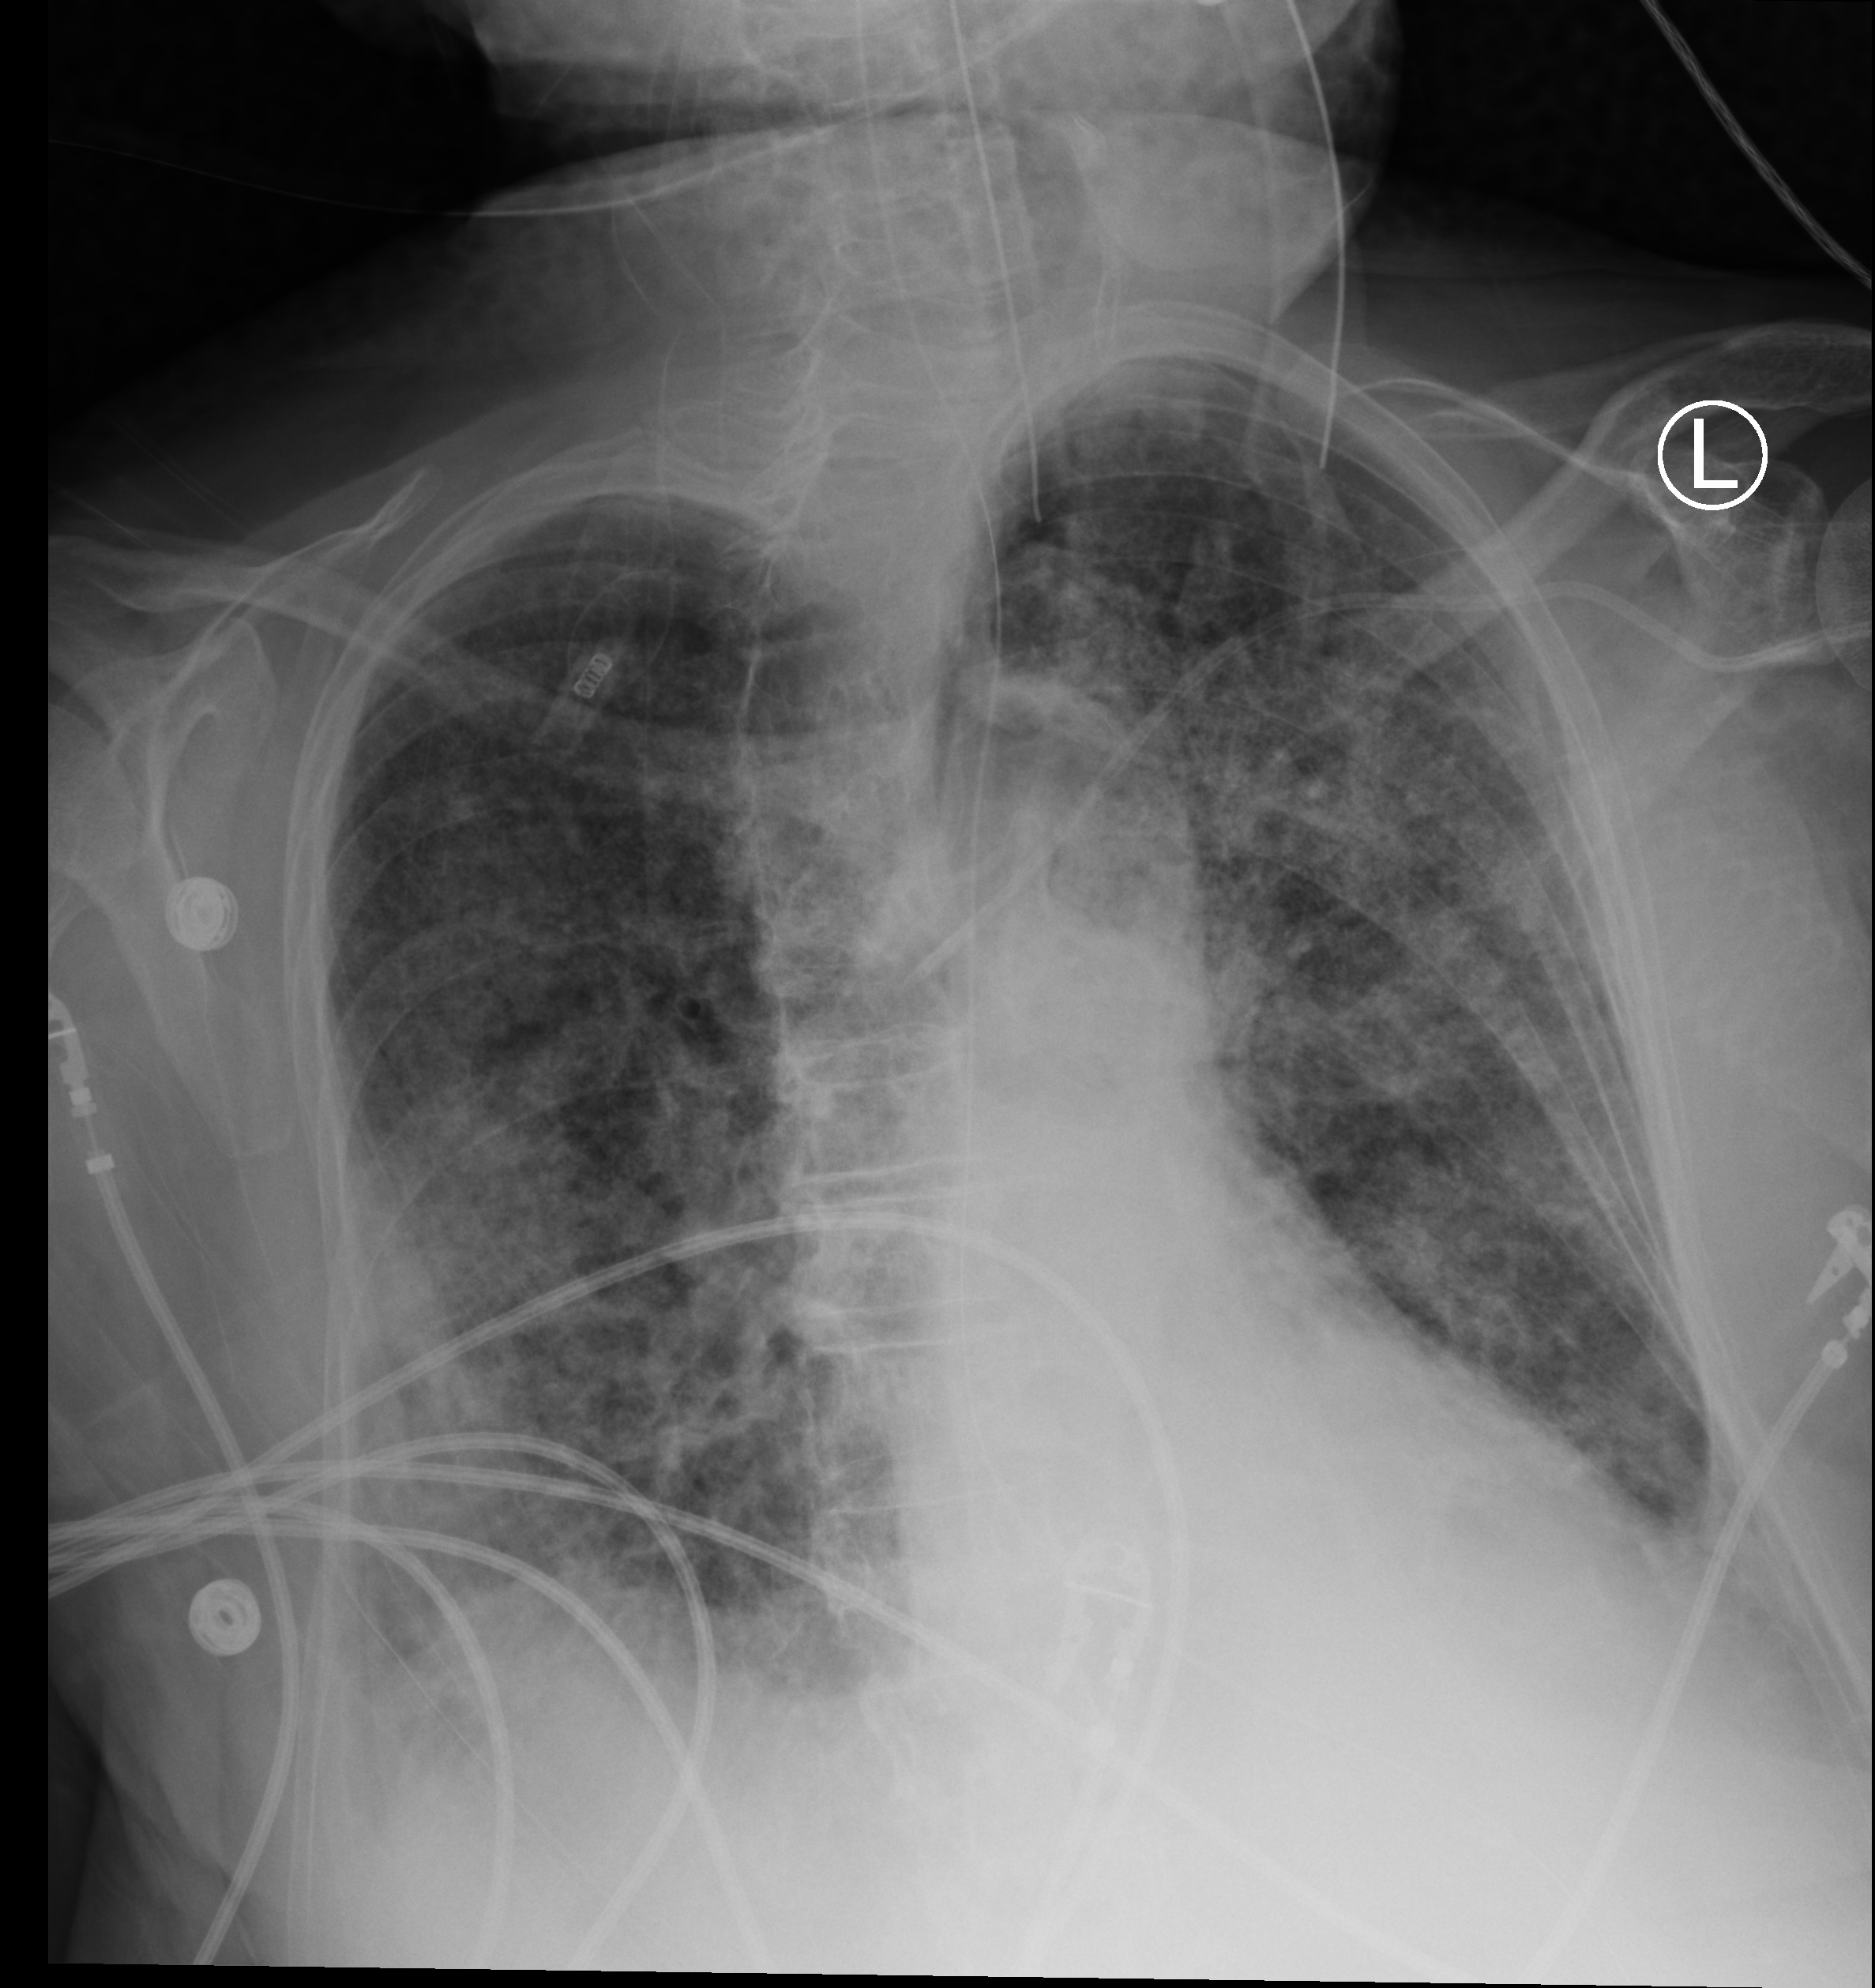
Chest X-ray (portable); anteroposterior (AP) projection. Patient hospitalised with COVID-19; female, aged 75–90 years.
From the hospital-stay record, not from the radiograph (when in the stay this image was taken is not recorded): diabetes (admission record): no.